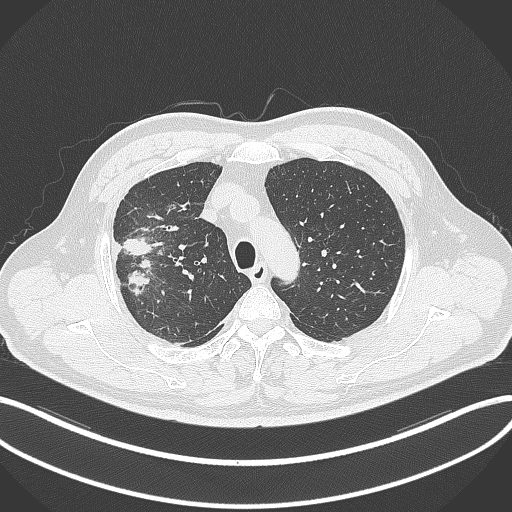
Chest CT, one axial slice. Position 264 of 348 along the scan axis. 120 kVp. Lung window (W 1500 / L -600 HU). 512 × 512 image matrix, field of view 400 × 400 mm. Patient: male, 55 years. Case-level facts recorded for this patient, not image findings: clinical TNM (as recorded): T3 N2 M1.
Outlined on this slice (rectangle marked by the reading radiologist):
- lung tumour (recorded histology: adenocarcinoma): bounding box [x1, y1, x2, y2] px = [117, 231, 155, 298]